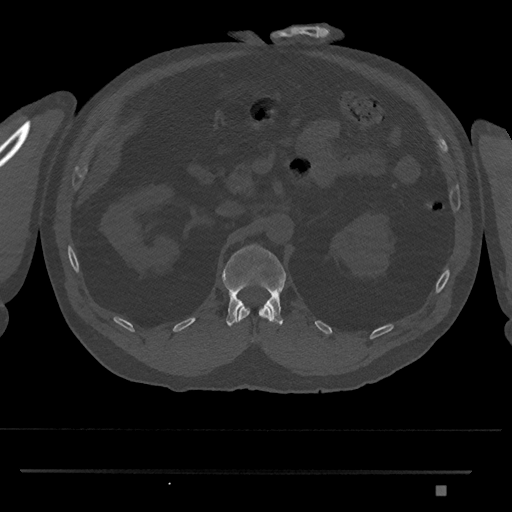
CT including the spine, one axial slice; position 847 of 1134 along the scan axis; reconstruction kernel Br40s/3; bone window (W 1800 / L 400 HU); 0.5 mm slice thickness; 512 × 512 image matrix, field of view 429 × 429 mm. Patient: male, 65 years. Case-level facts recorded for this patient, not image findings: primary cancer: prostate.
Outlined on this slice (semi-automatically segmented with operator editing):
- L1 vertebra: bounding box [x1, y1, x2, y2] px = [222, 244, 287, 327]
- T12 vertebra: [238, 305, 272, 341]